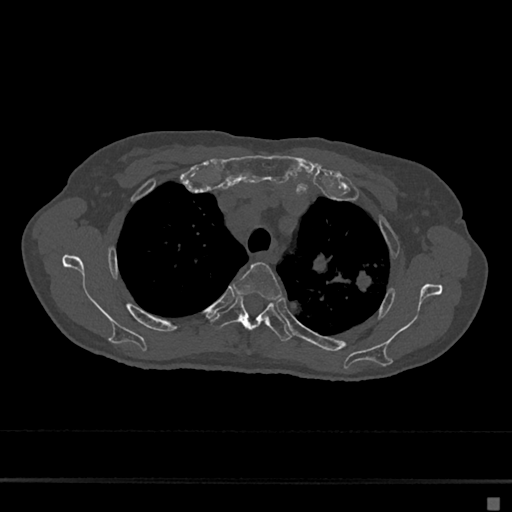
CT including the spine, one axial slice; slice 518 of 797 in the series (ordered by position); reconstruction kernel Br40s/3; 120 kVp; bone window (W 1800 / L 400 HU); 512 × 512 image matrix. Patient: female, 68 years. From the clinical record (not read from this slice): primary cancer: renal.
Structures marked on this image (semi-automatically segmented with operator editing):
- T3 vertebra: bounding box (x1, y1, x2, y2) in pixels: (231, 263, 282, 300)
- T4 vertebra: (210, 297, 291, 342)